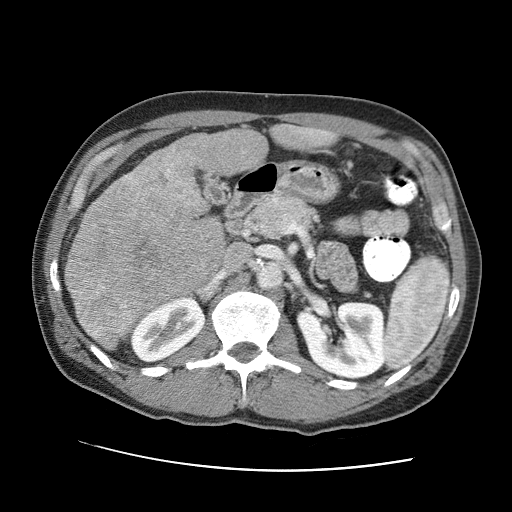
Contrast-enhanced abdominal CT (liver protocol), one axial slice. Position 36 of 95 along the scan axis. Reconstruction kernel STANDARD. 120 kVp. One of 2 acquisitions stored at this slice position. Soft-tissue window (W 400 / L 40 HU). 2.5 mm slice thickness. 512 × 512 image matrix, field of view 360 × 360 mm. From the clinical record (not read from this slice): diagnosis: hepatocellular carcinoma (patient treated with transarterial chemoembolisation; whether this scan precedes or follows treatment is not stated here); TNM stage (as recorded): Stage-IVA; Child-Pugh class: A.
Outlined on this slice (semi-automatic segmentation, software-assisted and operator-edited):
- liver parenchyma outside the tumour (the mass and vessels are separate outlines, so this box may not span the whole liver): bounding box [x1, y1, x2, y2] px = [64, 124, 320, 303]
- mass: [64, 143, 226, 350]
- liver vessels: [243, 129, 319, 153]